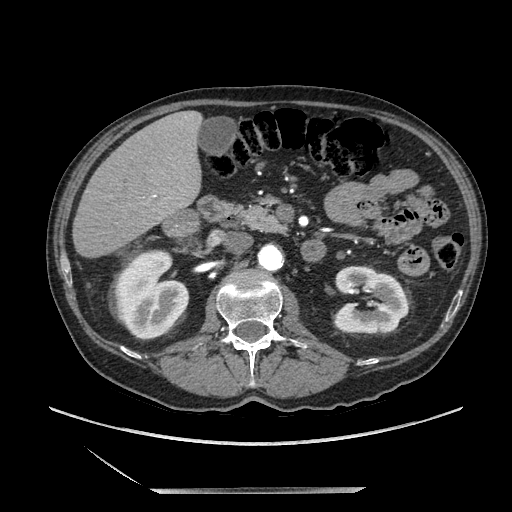
Contrast-enhanced abdominal CT, one axial slice; slice 93 of 243 in the series (ordered by position); soft-tissue window (W 400 / L 40 HU); 512 × 512 image matrix, field of view 420 × 420 mm. Male patient. From the clinical record (not read from this slice): diagnosis: adrenocortical carcinoma; tumour side: right adrenal; tumour size at pathology: 16 cm; Ki-67 index: 17 %; stage (as recorded): 3.
Annotated regions visible in this slice (semi-automatically segmented with operator editing):
- mass: bounding box <167,213,197,236> (left, top, right, bottom; pixels)